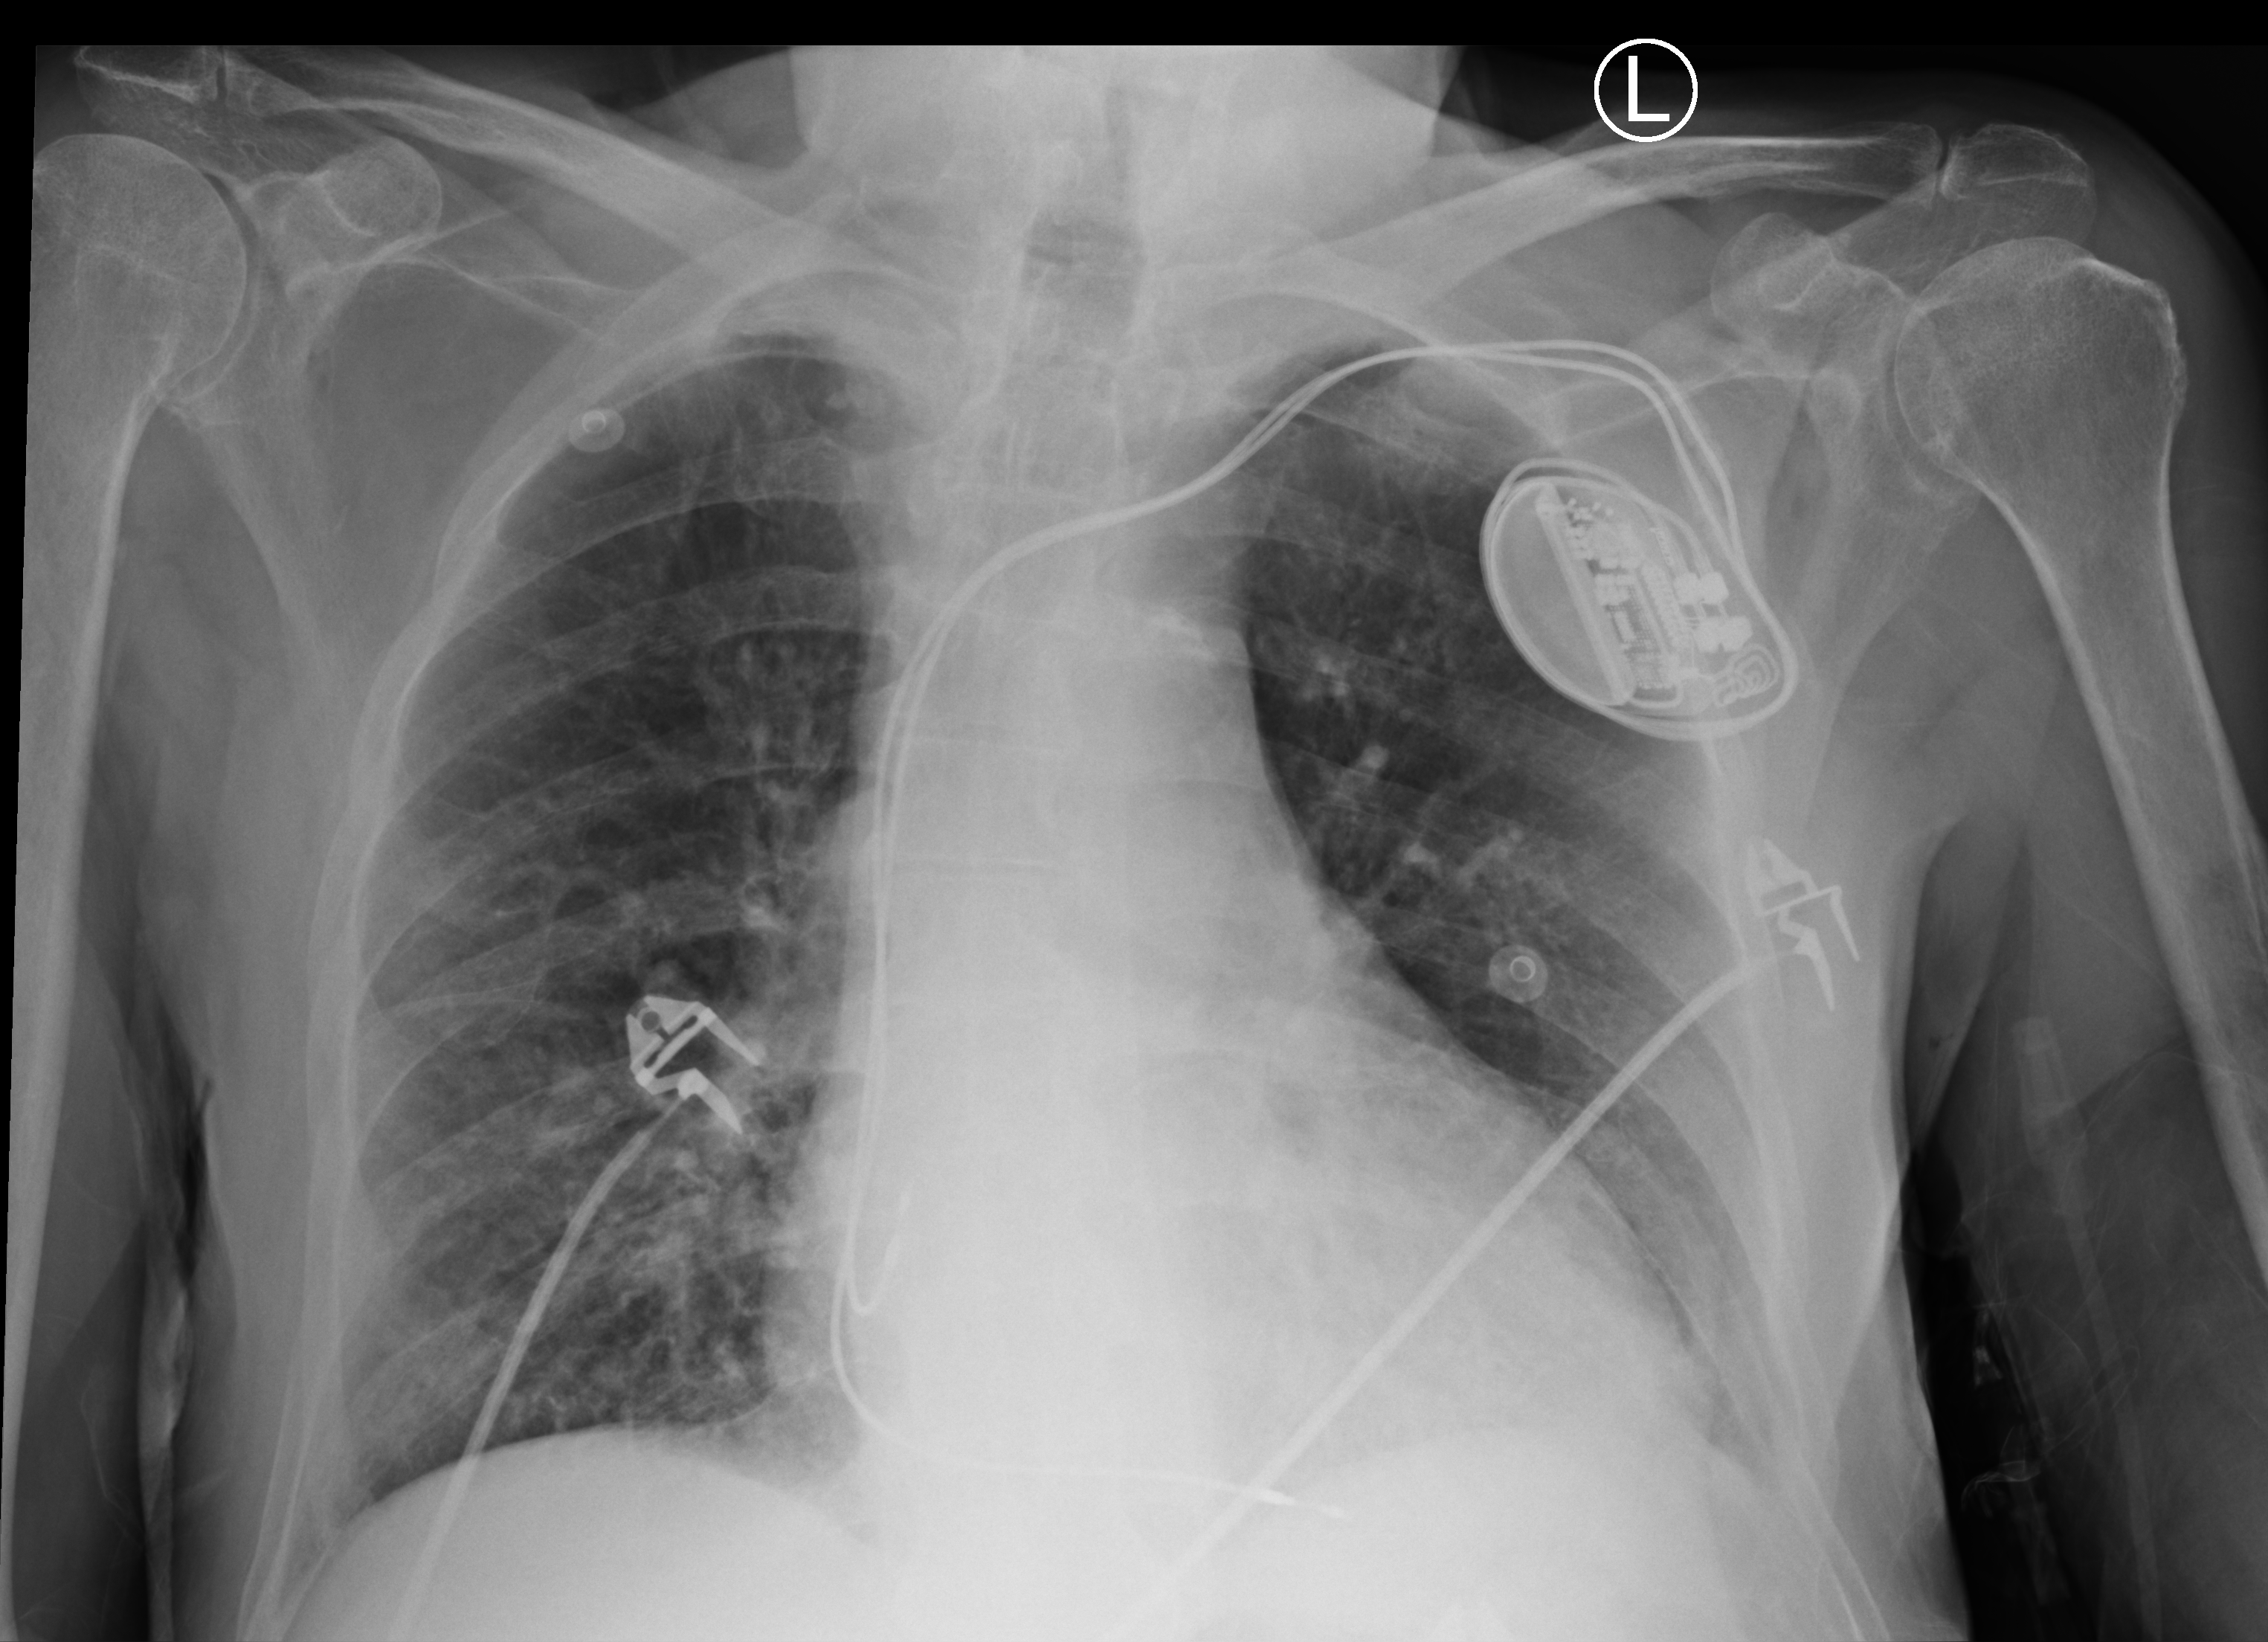
Chest X-ray (portable); anteroposterior (AP) projection. Male patient hospitalised with COVID-19, age 75–90 years.
Hospital-stay facts (about this admission, not read from this image; timing relative to this image not recorded):
- chronic kidney disease (admission record): no
- admitted to intensive care during this hospital stay: no
- COPD (admission record): no